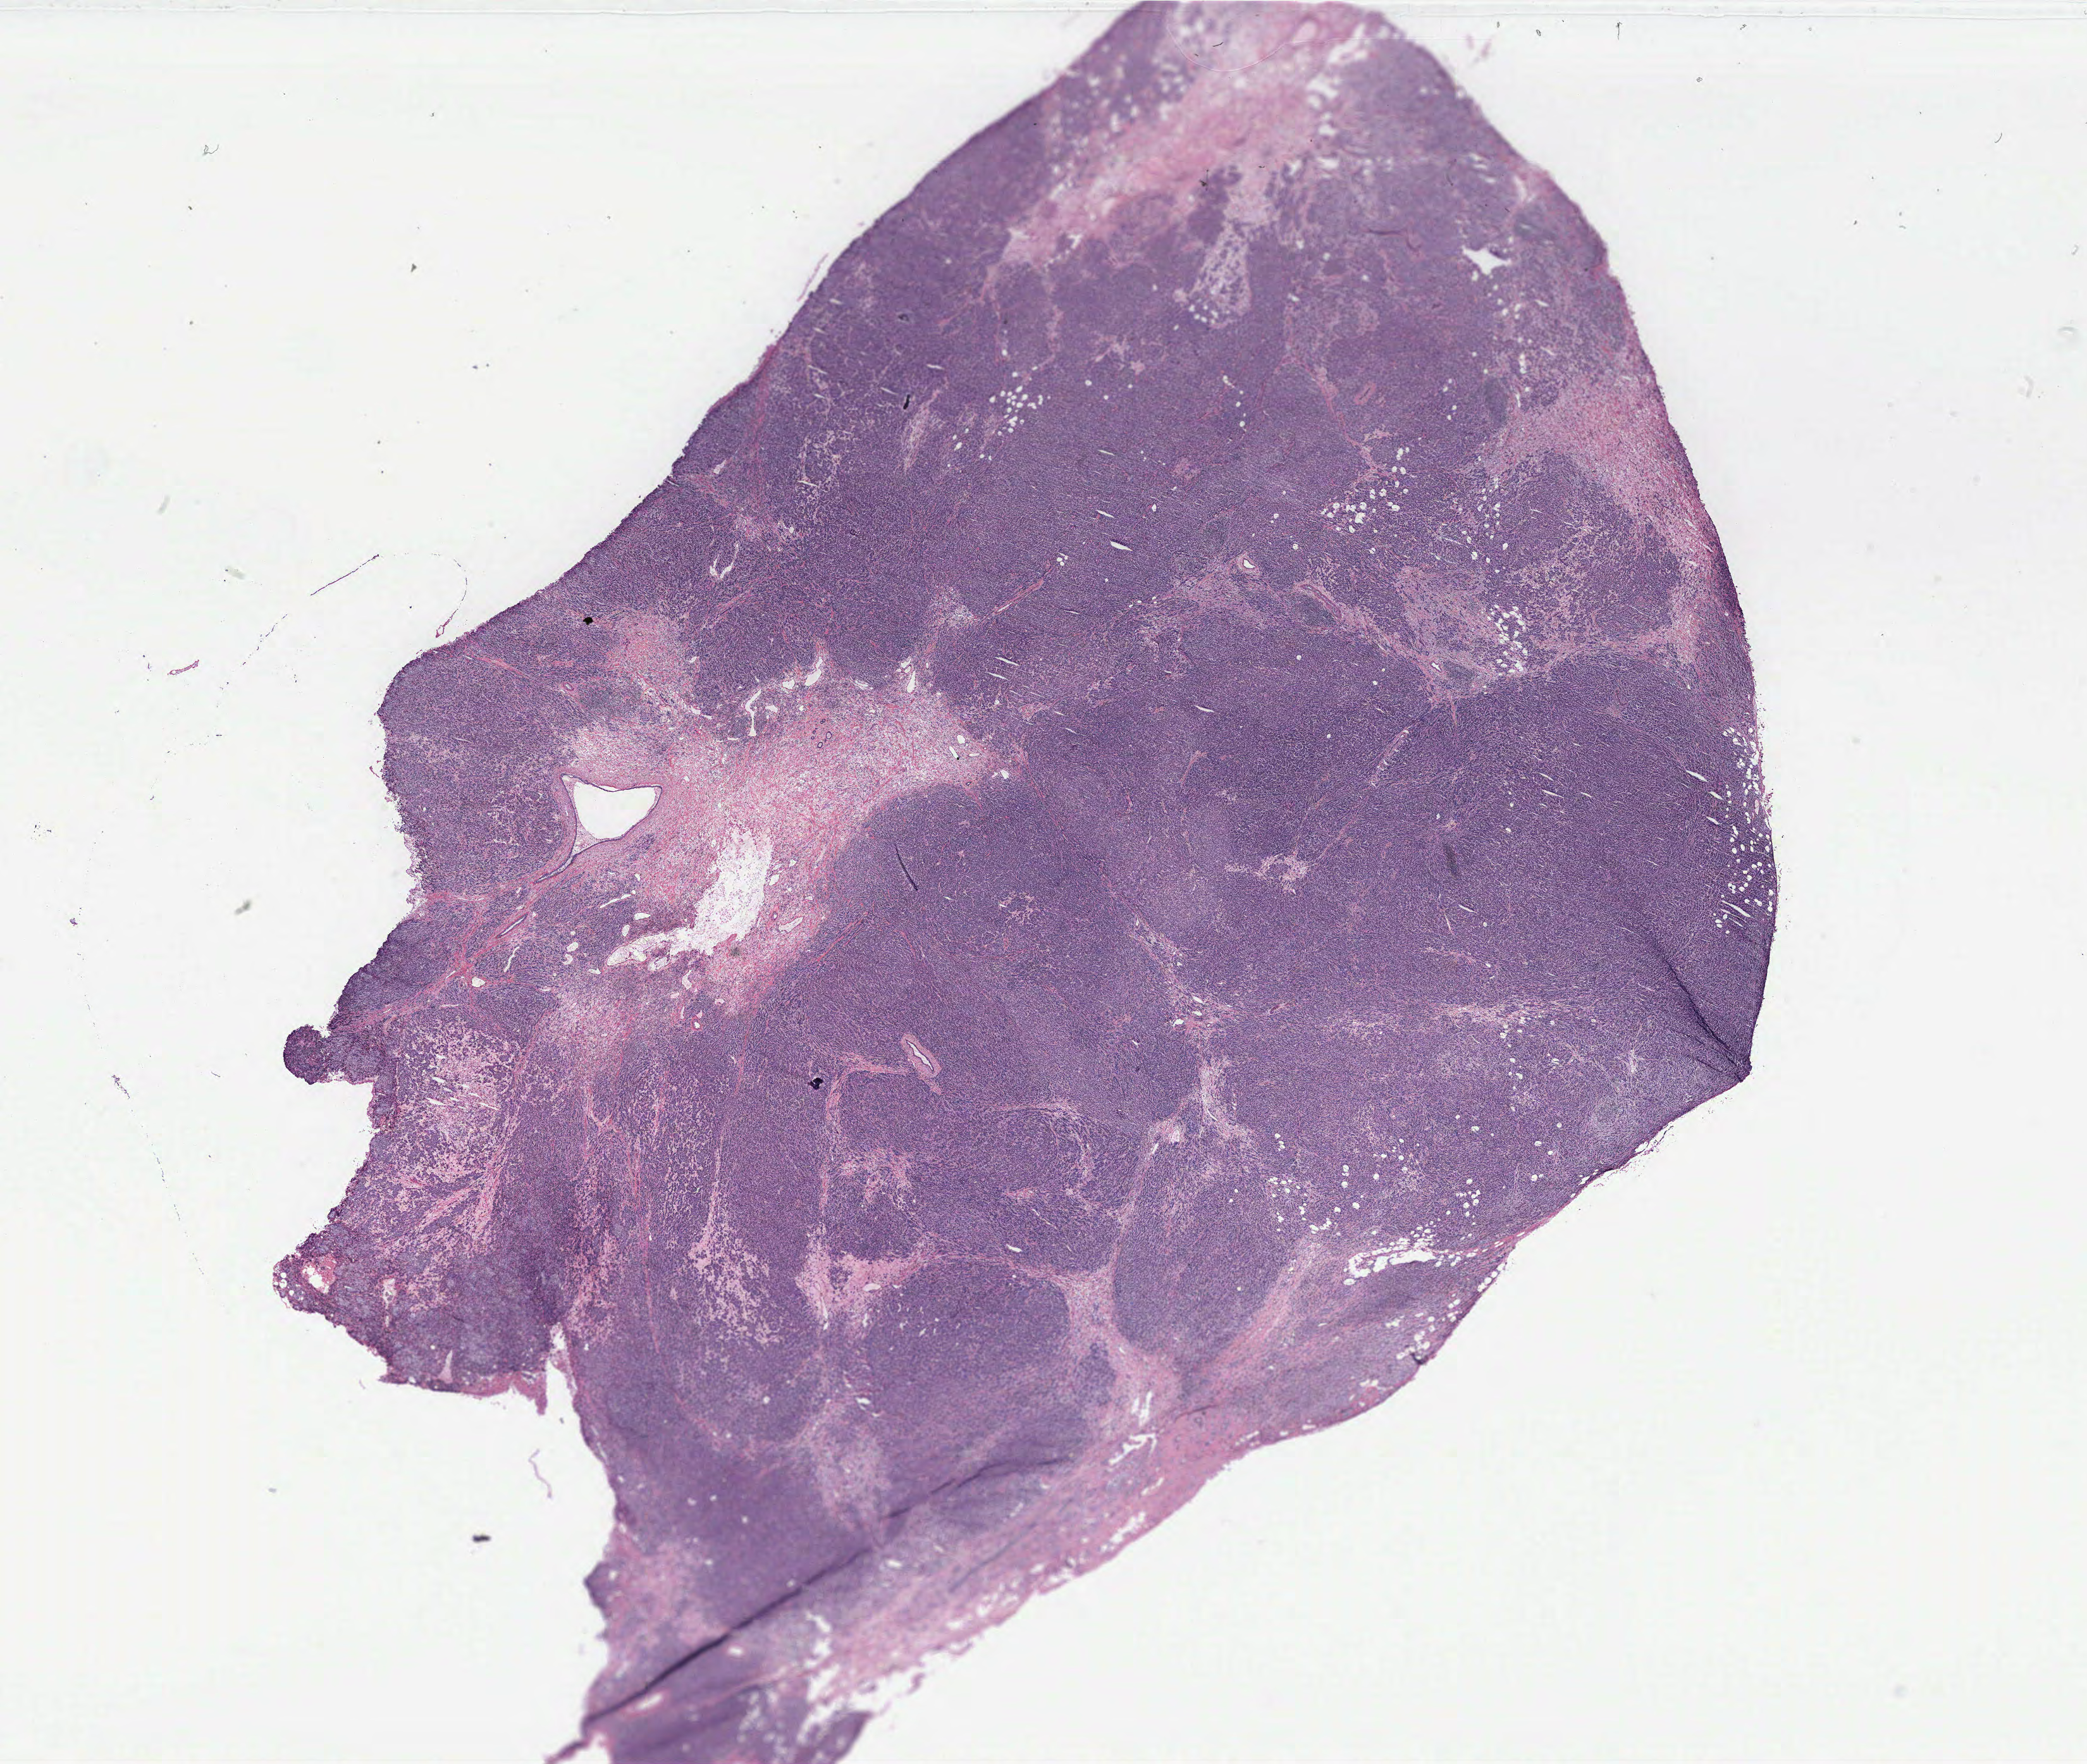
Digitized Hematoxylin and eosin (H&E) stained tissue section (whole slide) — low-resolution overview of the scanned area, about 26.4 x 22.3 mm (from a 40x scan), breast, tumour tissue. Female, 44 y/o.
- AJCC pathologic stage: IIIC
- diagnosis: Infiltrating duct carcinoma, NOS